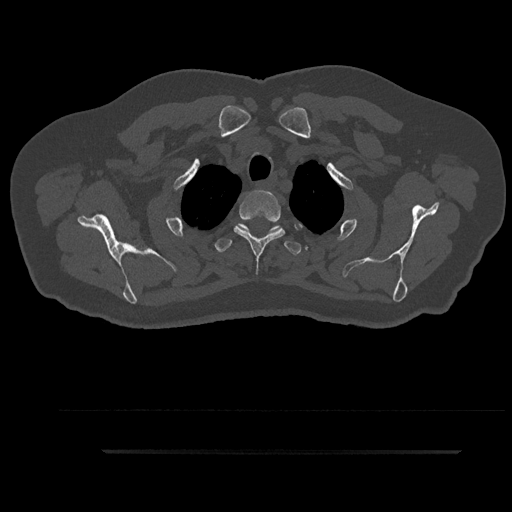
CT including the spine, one axial slice; position 749 of 797 along the scan axis; reconstruction kernel Br40s/3; bone window (W 1800 / L 400 HU); 0.5 mm slice thickness; 512 × 512 image matrix. Patient: male, 63 years. Case-level facts recorded for this patient, not image findings: primary cancer: renal.
Outlined on this slice (semi-automatically segmented with operator editing):
- T2 vertebra: bounding box (x1, y1, x2, y2) in pixels: (234, 190, 298, 264)
- T3 vertebra: (215, 223, 302, 255)